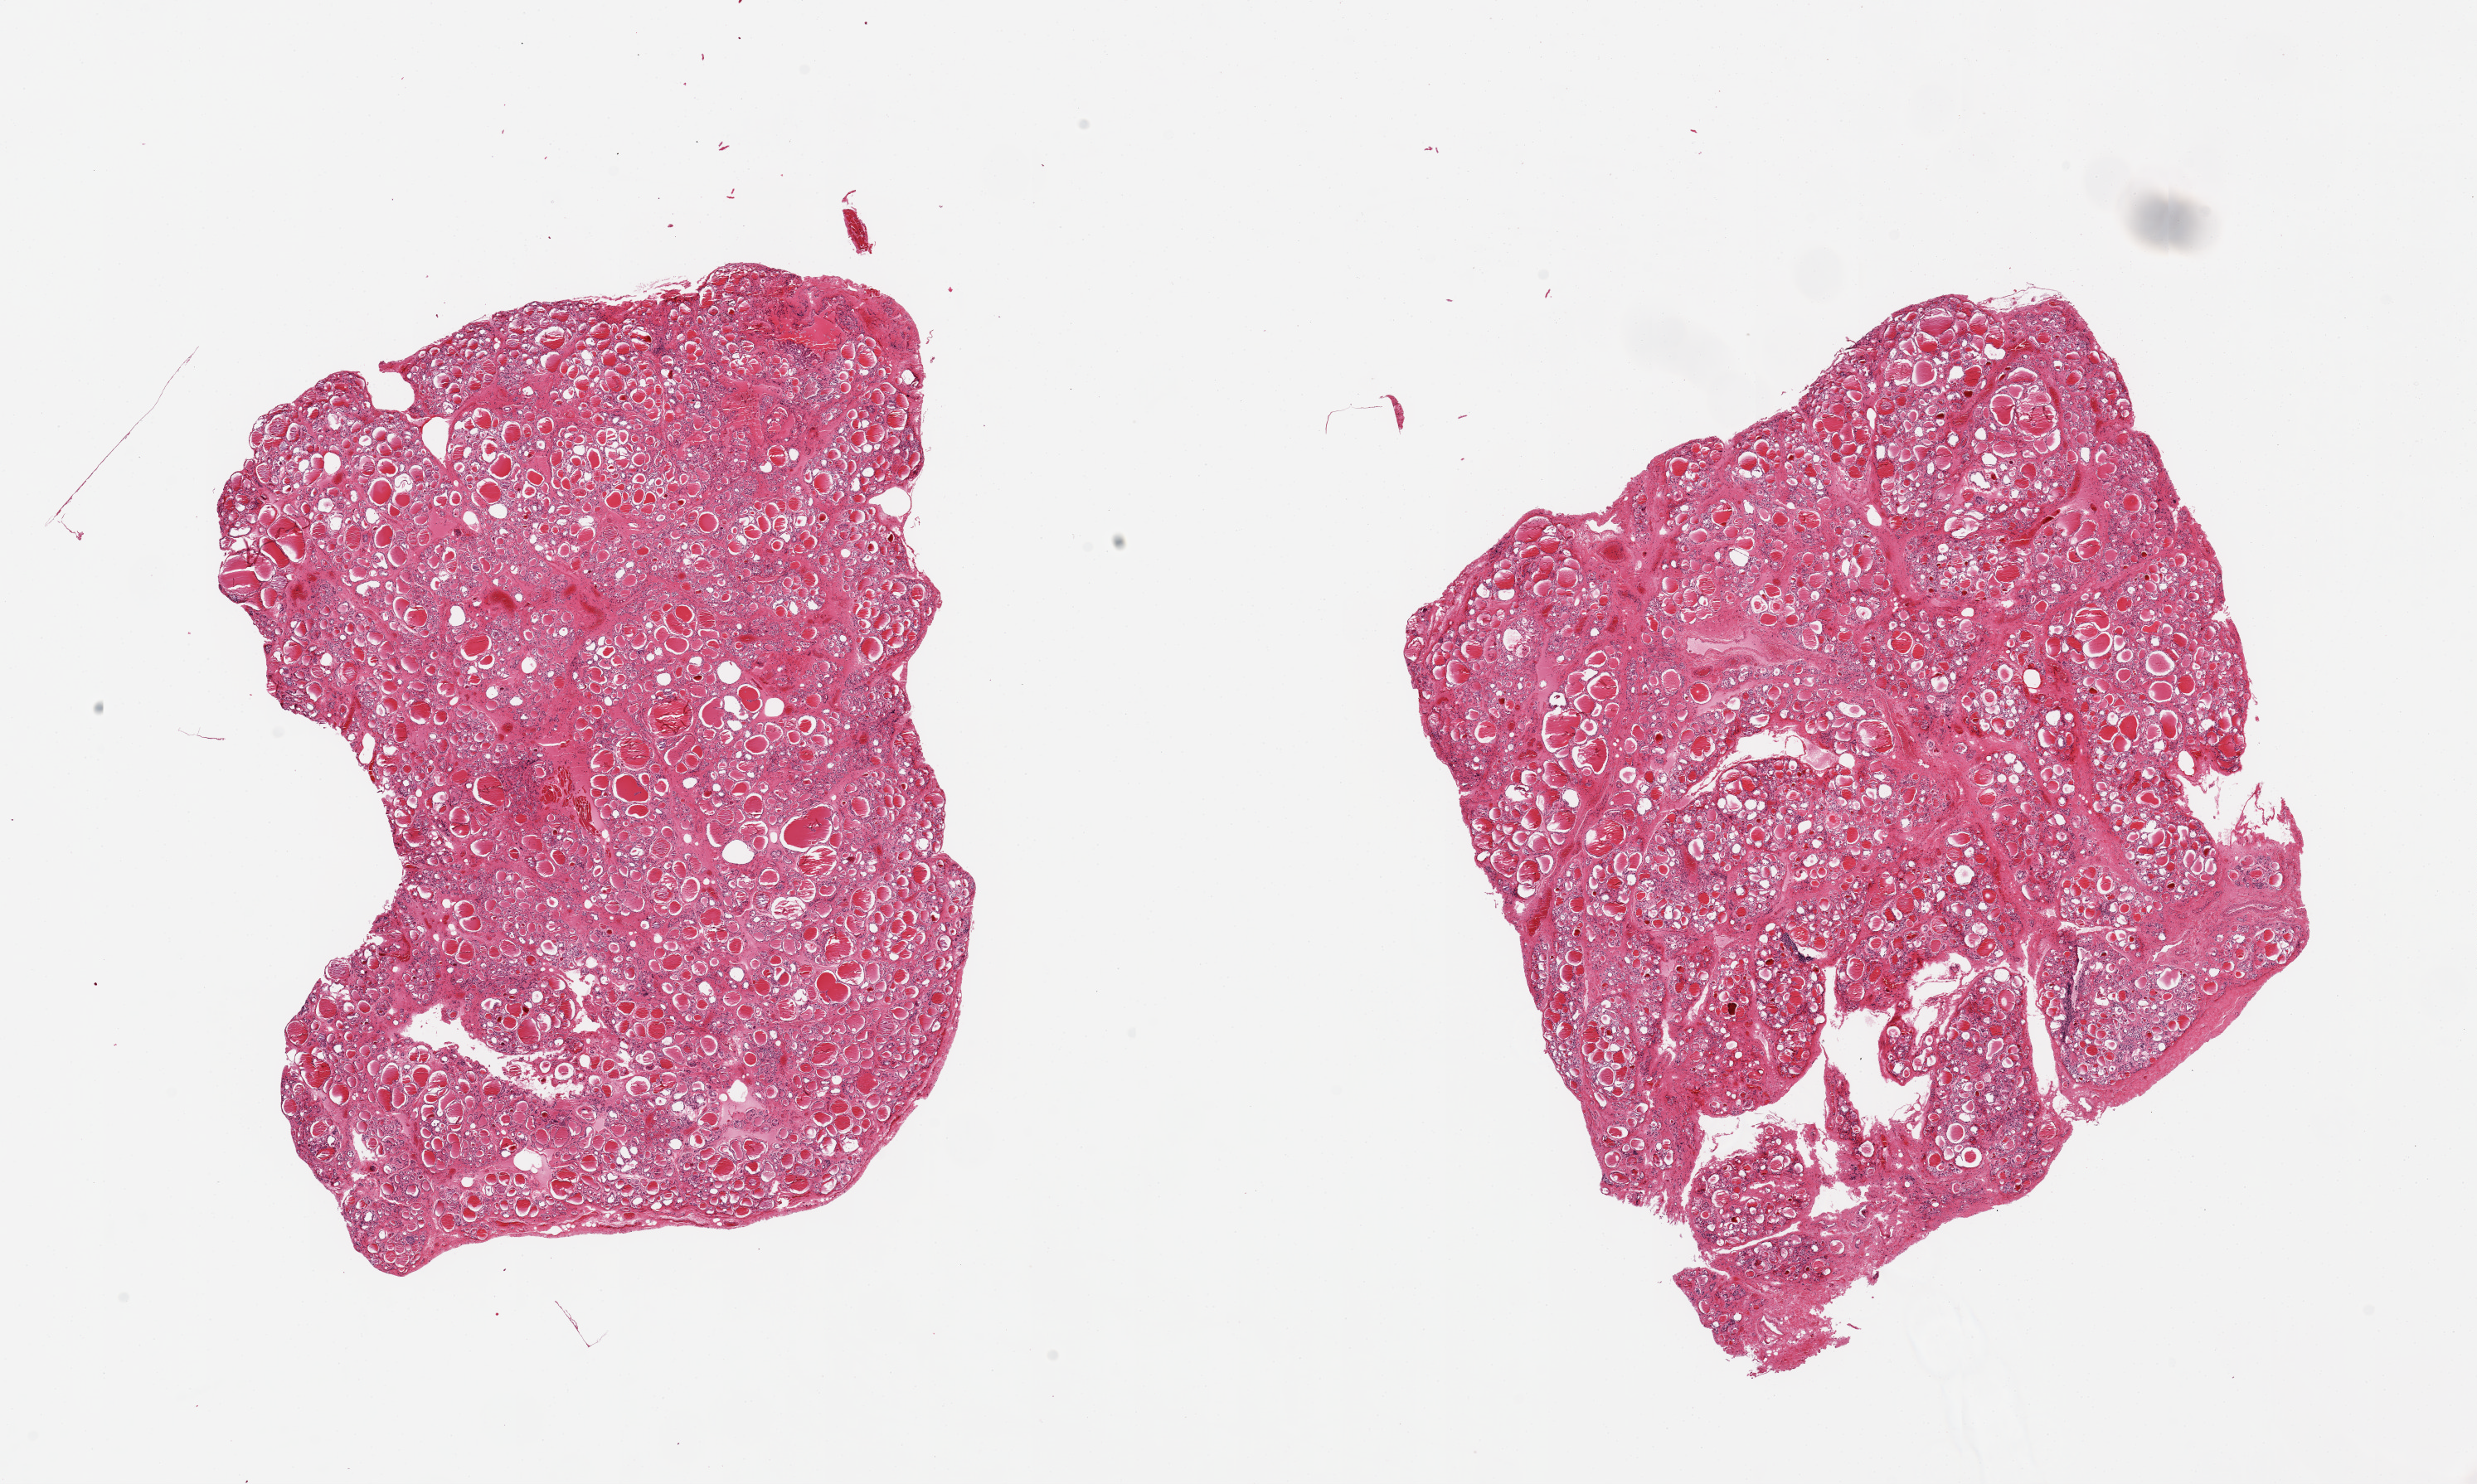
Hematoxylin and eosin (H&E) whole-slide image, low-resolution overview of the scanned area, about 23.6 x 14.2 mm, PAXgene-fixed, paraffin-embedded tissue, target tissue: thyroid, tissue donor sample. Donor: male.
Reviewer comment on this tissue sample: 2 pieces 9.5x7 & 8x8mm.